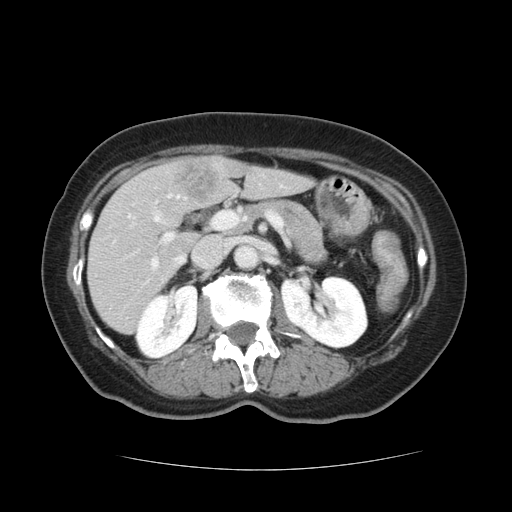
Contrast-enhanced abdominal CT, one axial slice; slice 59 of 128 in the series (ordered by position); intravenous contrast given; soft-tissue window (W 400 / L 40 HU); 2.5 mm slice thickness; 512 × 512 image matrix, field of view 366 × 366 mm. Female patient, age 67 years. Case-level facts recorded for this patient, not image findings: diagnosis: colorectal cancer liver metastases, imaged before liver resection; multiple liver metastases: yes; largest metastasis: 3 cm; disease in both lobes: yes.
Structures marked on this image (outlined manually by an expert reader):
- hepatic veins: bounding box [x1, y1, x2, y2] px = [174, 255, 184, 265]
- liver: [88, 158, 310, 333]
- planned liver remnant (the part of the liver to remain after resection): [88, 166, 310, 334]
- portal vein (with intrahepatic branches): [112, 212, 235, 270]
- liver metastasis: [177, 164, 218, 202]